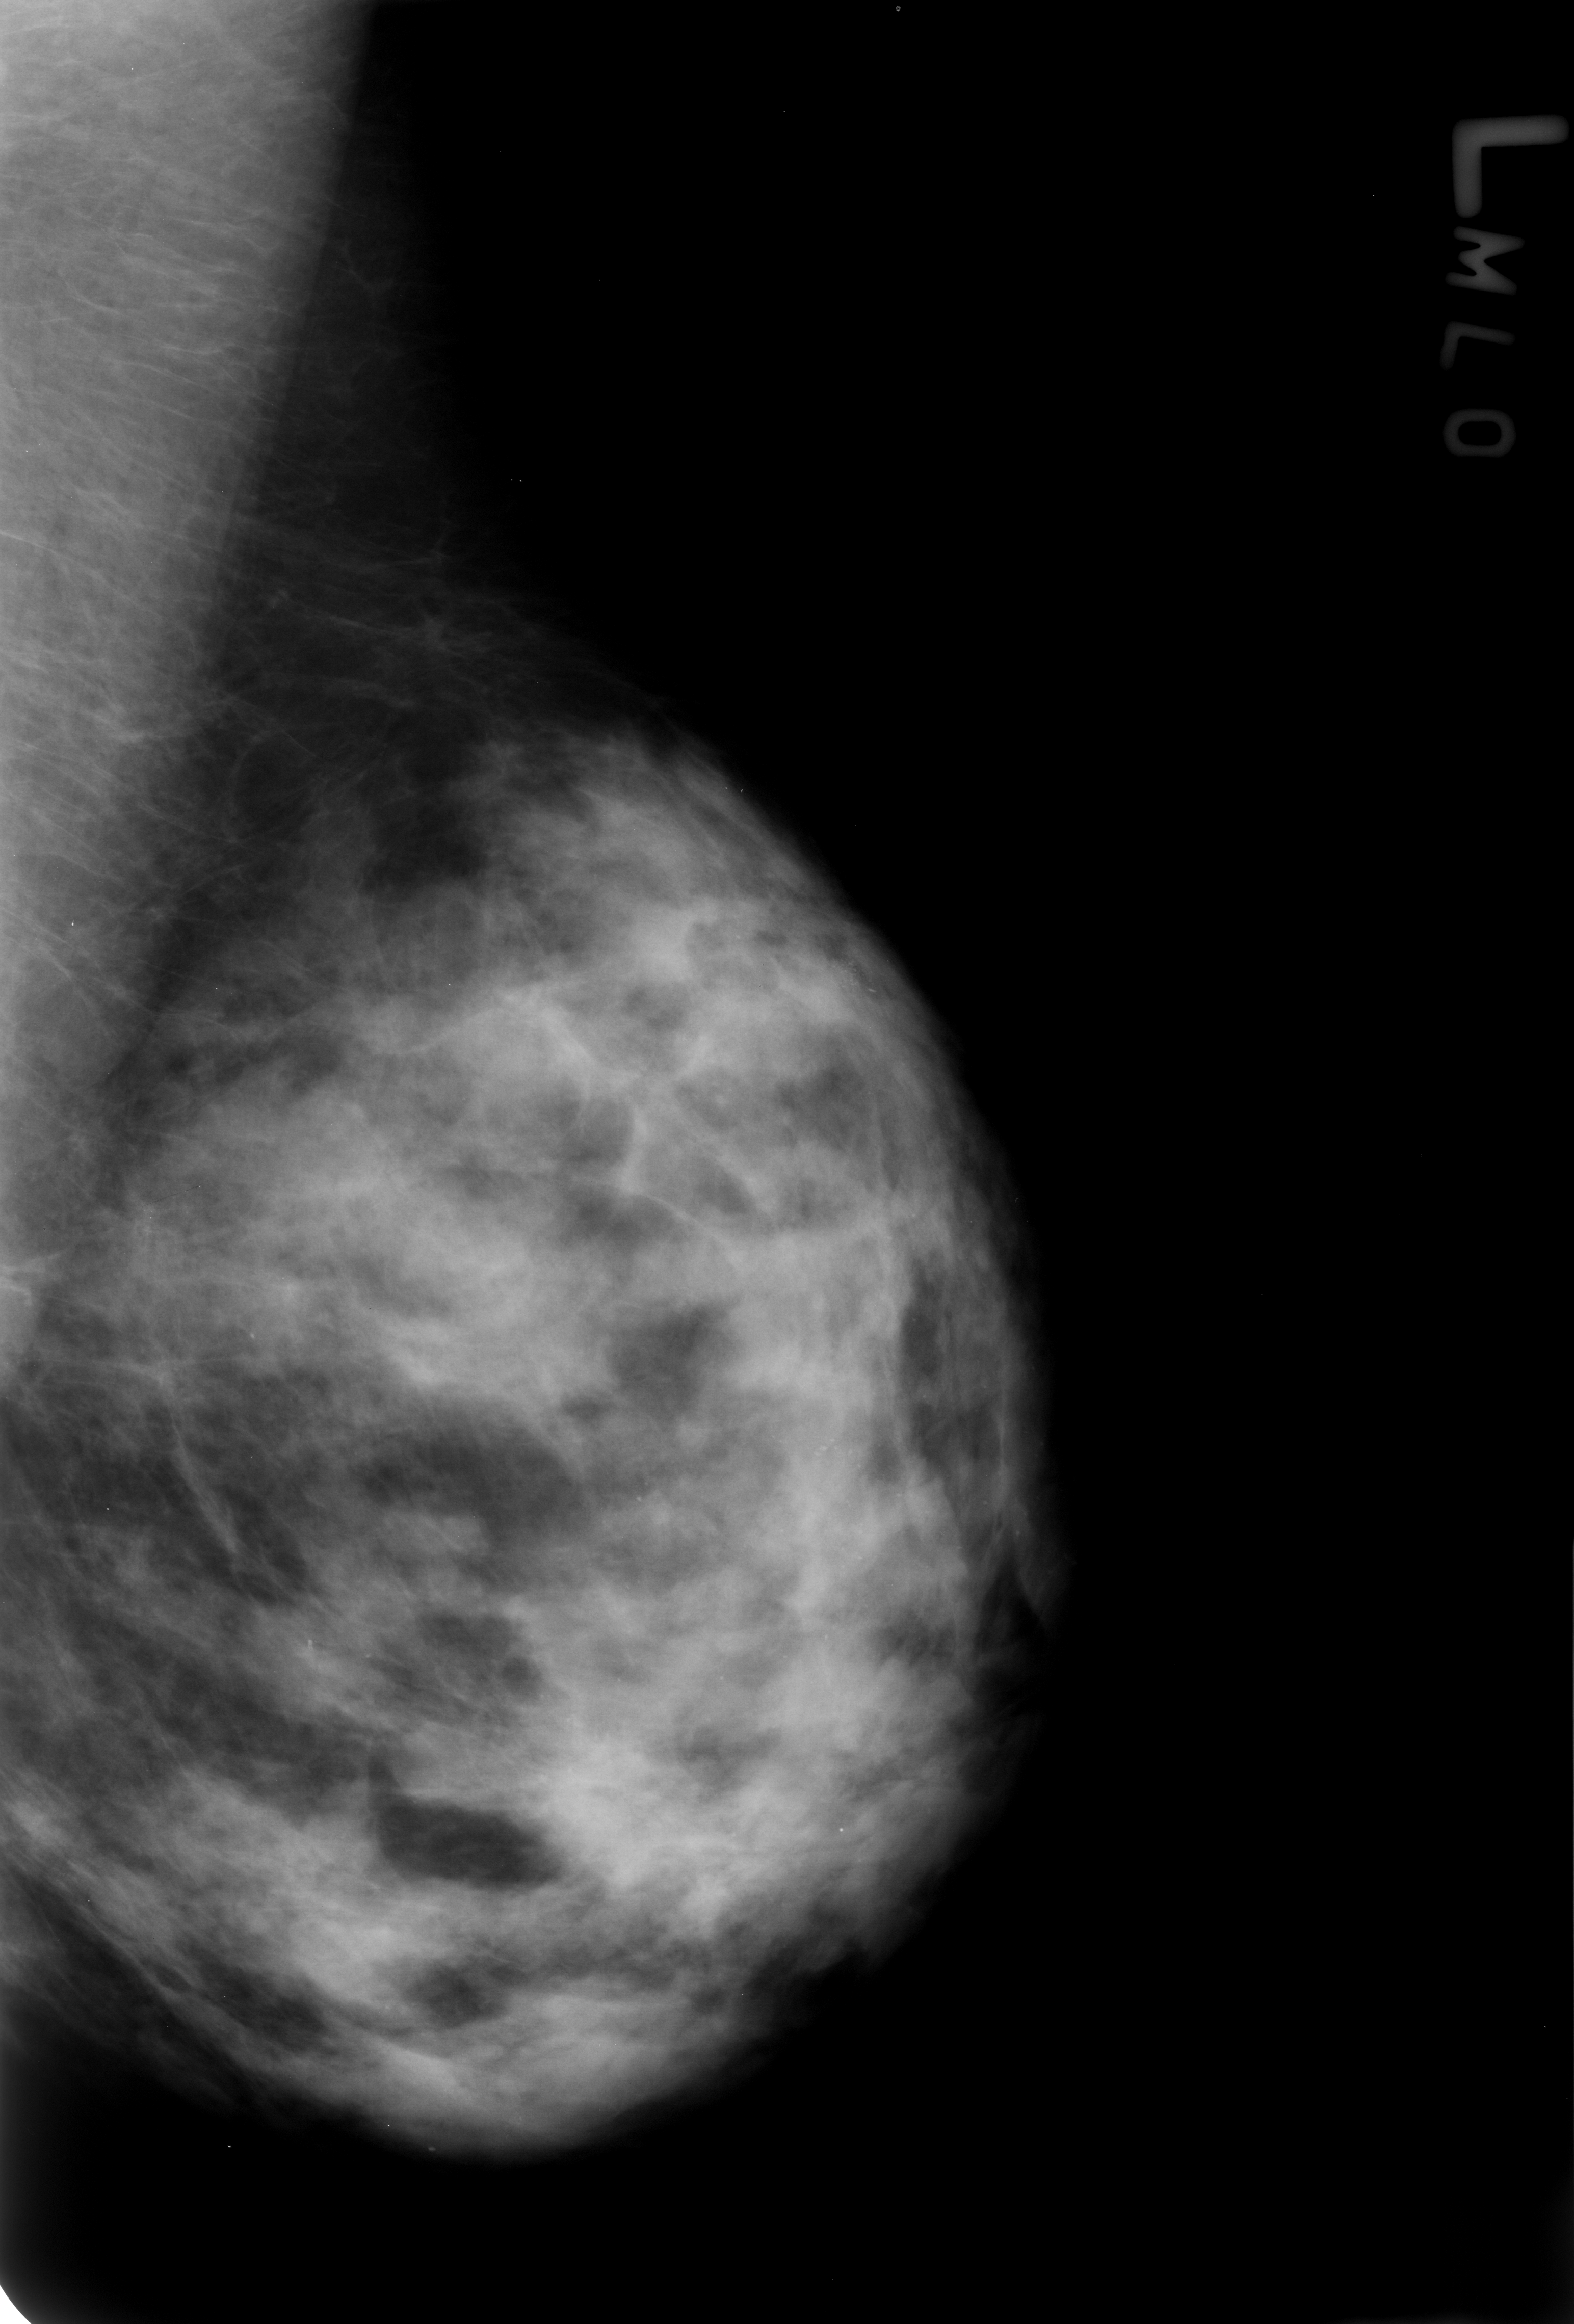
Scanned film-screen mammogram; left breast; MLO view; BI-RADS breast density category 3 (scale 1–4); 1574 × 2324 image matrix.
Expert-marked regions of interest on this image (one box per marked abnormality):
- calcifications, morphology pleomorphic, distribution clustered; BI-RADS assessment category 4; subtlety rating 2 on a 1 (subtle) to 5 (obvious) scale; pathology result (as recorded, not read from the image): benign: bounding box <815,949,902,1041> (left, top, right, bottom; pixels)